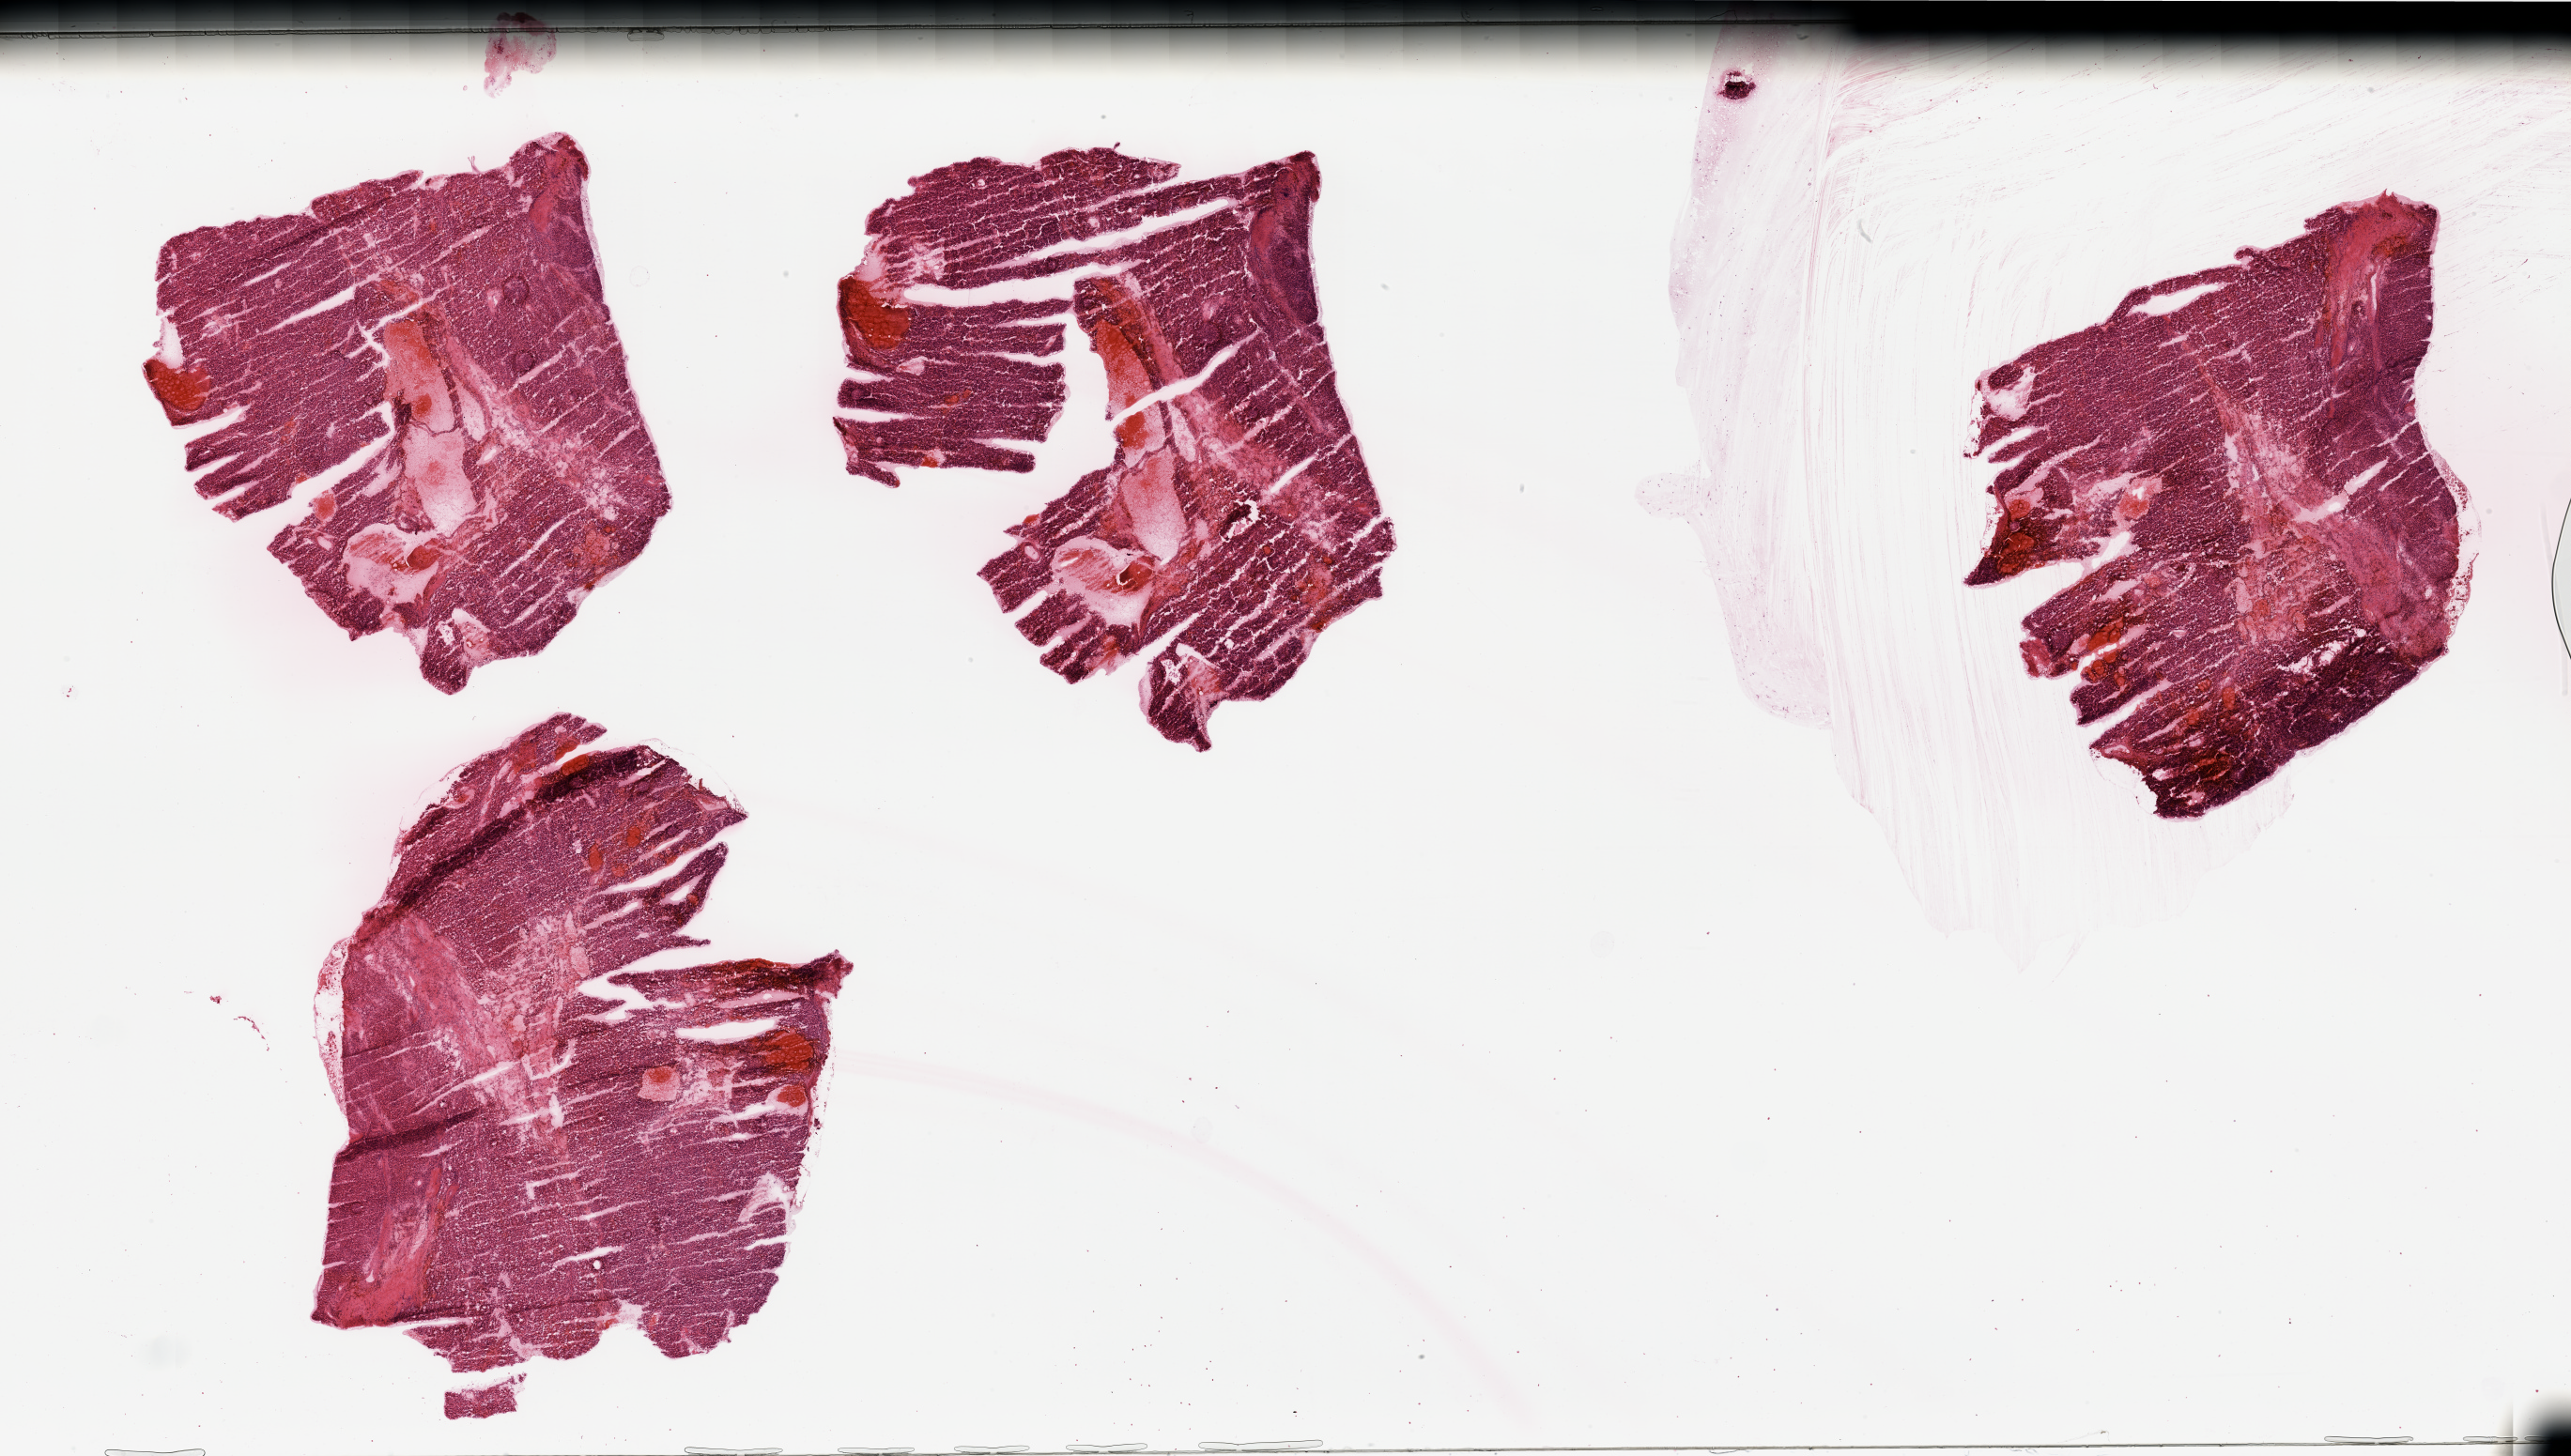
Whole-slide histology image, H&E, whole scanned area (about 43.3 x 24.5 mm, slide scanned at 20x) shown as a low-resolution overview; tumour tissue sample, sampled site: kidney. Male, 66 y/o. Histologic grade: G2 (moderately differentiated). Pathologist review of this section (percent, as recorded): tumour nuclei 85%, necrosis 10%.
Primary tumour site (as recorded): upper pole. Histologic diagnosis: Renal cell carcinoma, NOS. AJCC pathologic stage: I.